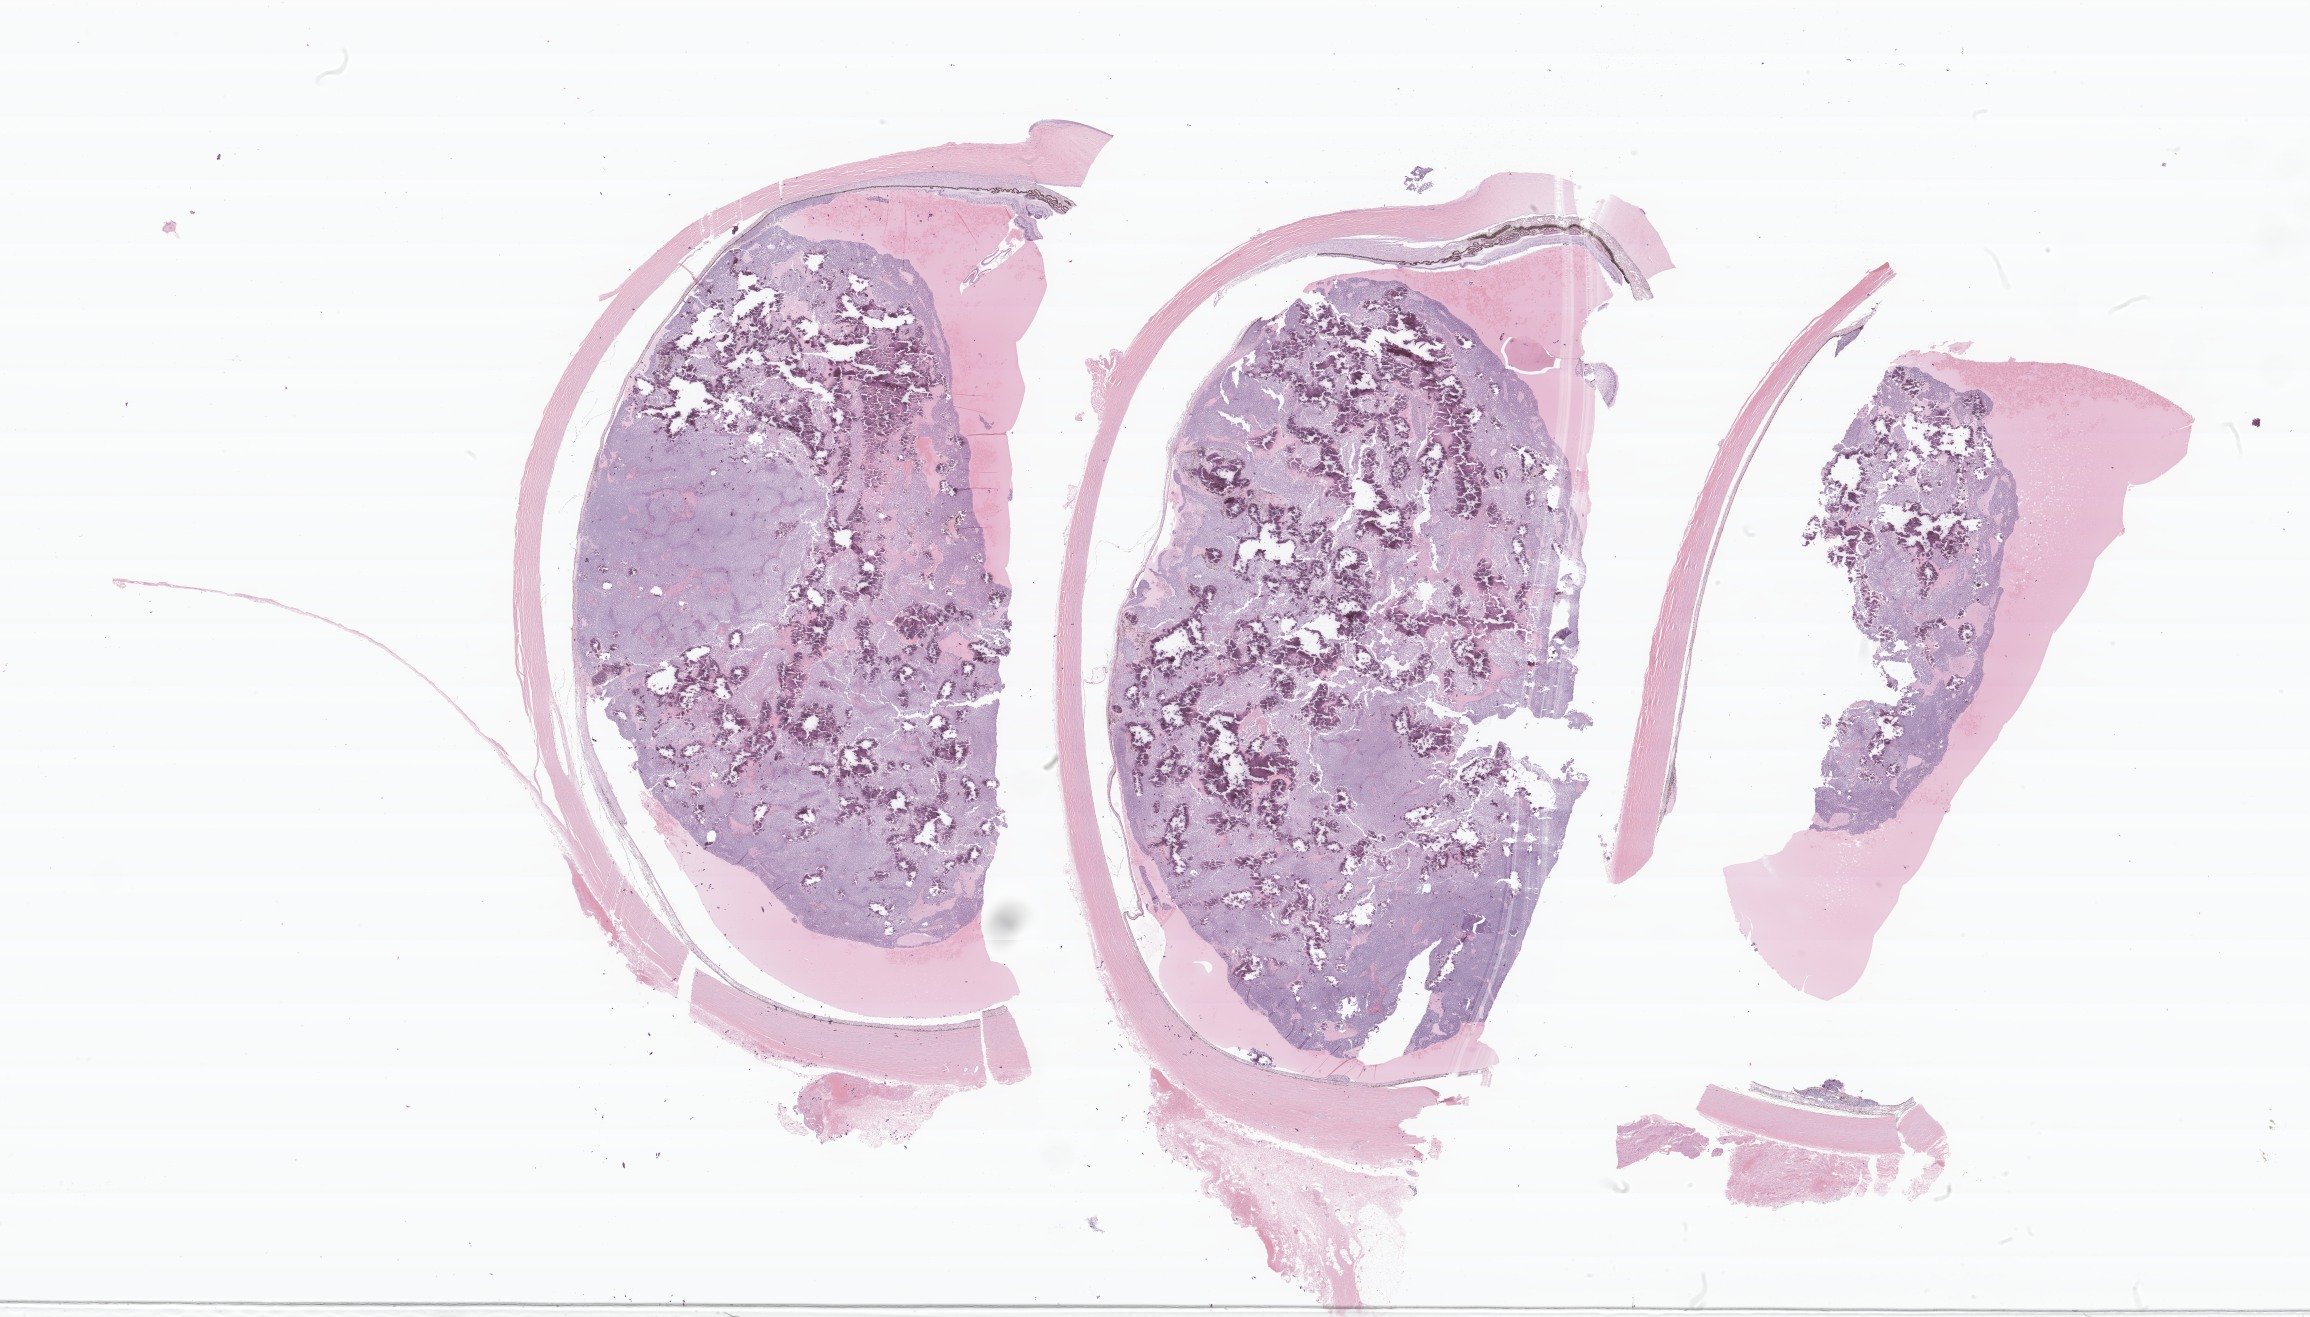
Digitized haematoxylin and eosin-stained section of tumor tissue from the eye — shown as a low-resolution overview of the whole scanned area (about 38.9 x 22.2 mm), formalin-fixed, paraffin-embedded (FFPE) tissue. Patient: male, age 342 days.
• diagnosis (ICD-O-3 morphology term): Retinoblastoma, NOS